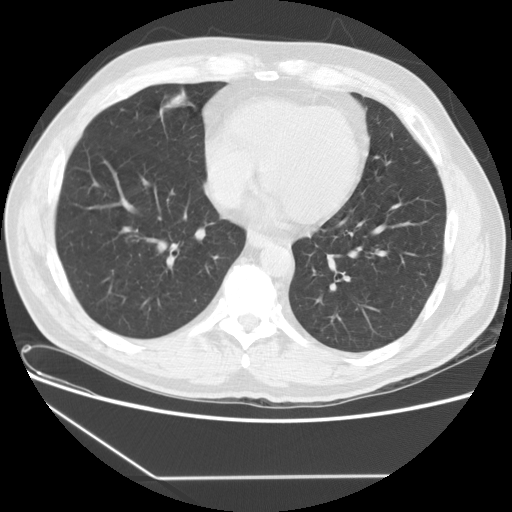
Low-dose screening chest CT, axial slice, baseline screening round, lung window (W 1500 / L -600 HU), 2.5 mm slice thickness, slice 102 of 154 in the series. Male participant, aged 59 years at enrolment.
Lesion marked by an expert reader, bounding box [x1, y1, x2, y2] px = [154, 87, 198, 117]. Screening reader's record for this exam: no non-calcified nodule ≥4 mm recorded. Official screen result: positive, change unspecified: nodule(s) >= 4 mm or enlarging nodule(s), mass(es), or other non-specific abnormalities suspicious for lung cancer. Lung cancer was diagnosed 58 days after this screen: oat cell carcinoma, right middle lobe, stage IIA (AJCC 6th edition), 15 mm at pathology.